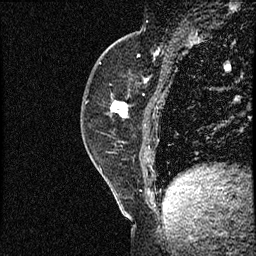
Breast MRI (dynamic contrast-enhanced), one sagittal slice. Slice 23 of 56 in the series (ordered by position). Dynamic contrast-enhanced study with each time point stored as its own series, time point 2 of 3 at this slice position (early post-contrast, ordered by acquisition time). 1.5 T. TE 4.2 ms, TR 17.3 ms. 2 mm slice thickness. 256 × 256 image matrix, field of view 200 × 200 mm. Female patient. Case-level facts recorded for this patient, not image findings: setting: breast cancer imaged before/during neoadjuvant chemotherapy; receptor status: HER2-positive.
Outlined on this slice (semi-automatic segmentation, software-assisted and operator-edited):
- analysis volume of interest (the breast-tissue region the enhancement analysis was run in; not a lesion): bounding box (x1, y1, x2, y2) in pixels: (81, 50, 156, 155)
- tumour enhancement mask (voxels above the 100 % enhancement threshold inside the analysis volume of interest): (111, 102, 128, 118)